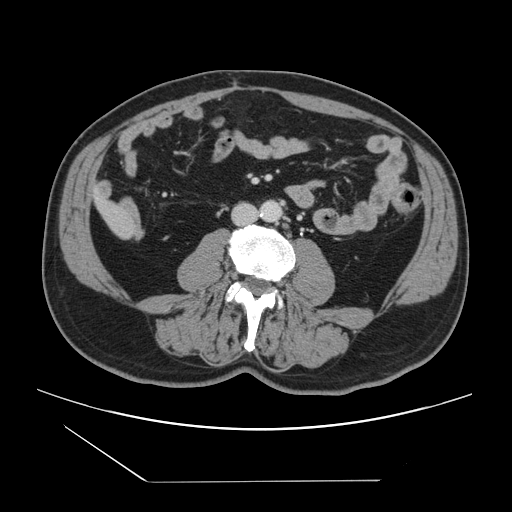
Contrast-enhanced abdominal CT, one axial slice. Position 14 of 157 along the scan axis. 120 kVp. Intravenous contrast given. Soft-tissue window (W 400 / L 40 HU). 2.5 mm slice thickness. 512 × 512 image matrix. Male patient, age 61 years. From the clinical record (not read from this slice): diagnosis: colorectal cancer liver metastases, imaged before liver resection; multiple liver metastases: yes.
Structures marked on this image (manually delineated by an expert):
- liver: bounding box (x1, y1, x2, y2) in pixels: (97, 199, 134, 238)
- planned liver remnant (the part of the liver to remain after resection): (97, 198, 119, 217)